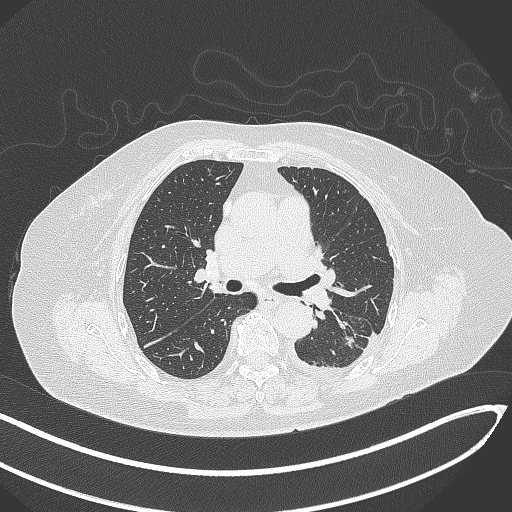
Chest CT, one axial slice; position 188 of 270 along the scan axis; 120 kVp; lung window (W 1500 / L -600 HU); 1 mm slice thickness; 512 × 512 image matrix, field of view 400 × 400 mm. Female patient, age 76 years. From the clinical record (not read from this slice): clinical TNM (as recorded): T1c N0 M0.
Annotated regions visible in this slice (rectangle marked by the reading radiologist):
- lung tumour (recorded histology: adenocarcinoma): bounding box [x1, y1, x2, y2] px = [343, 334, 359, 350]